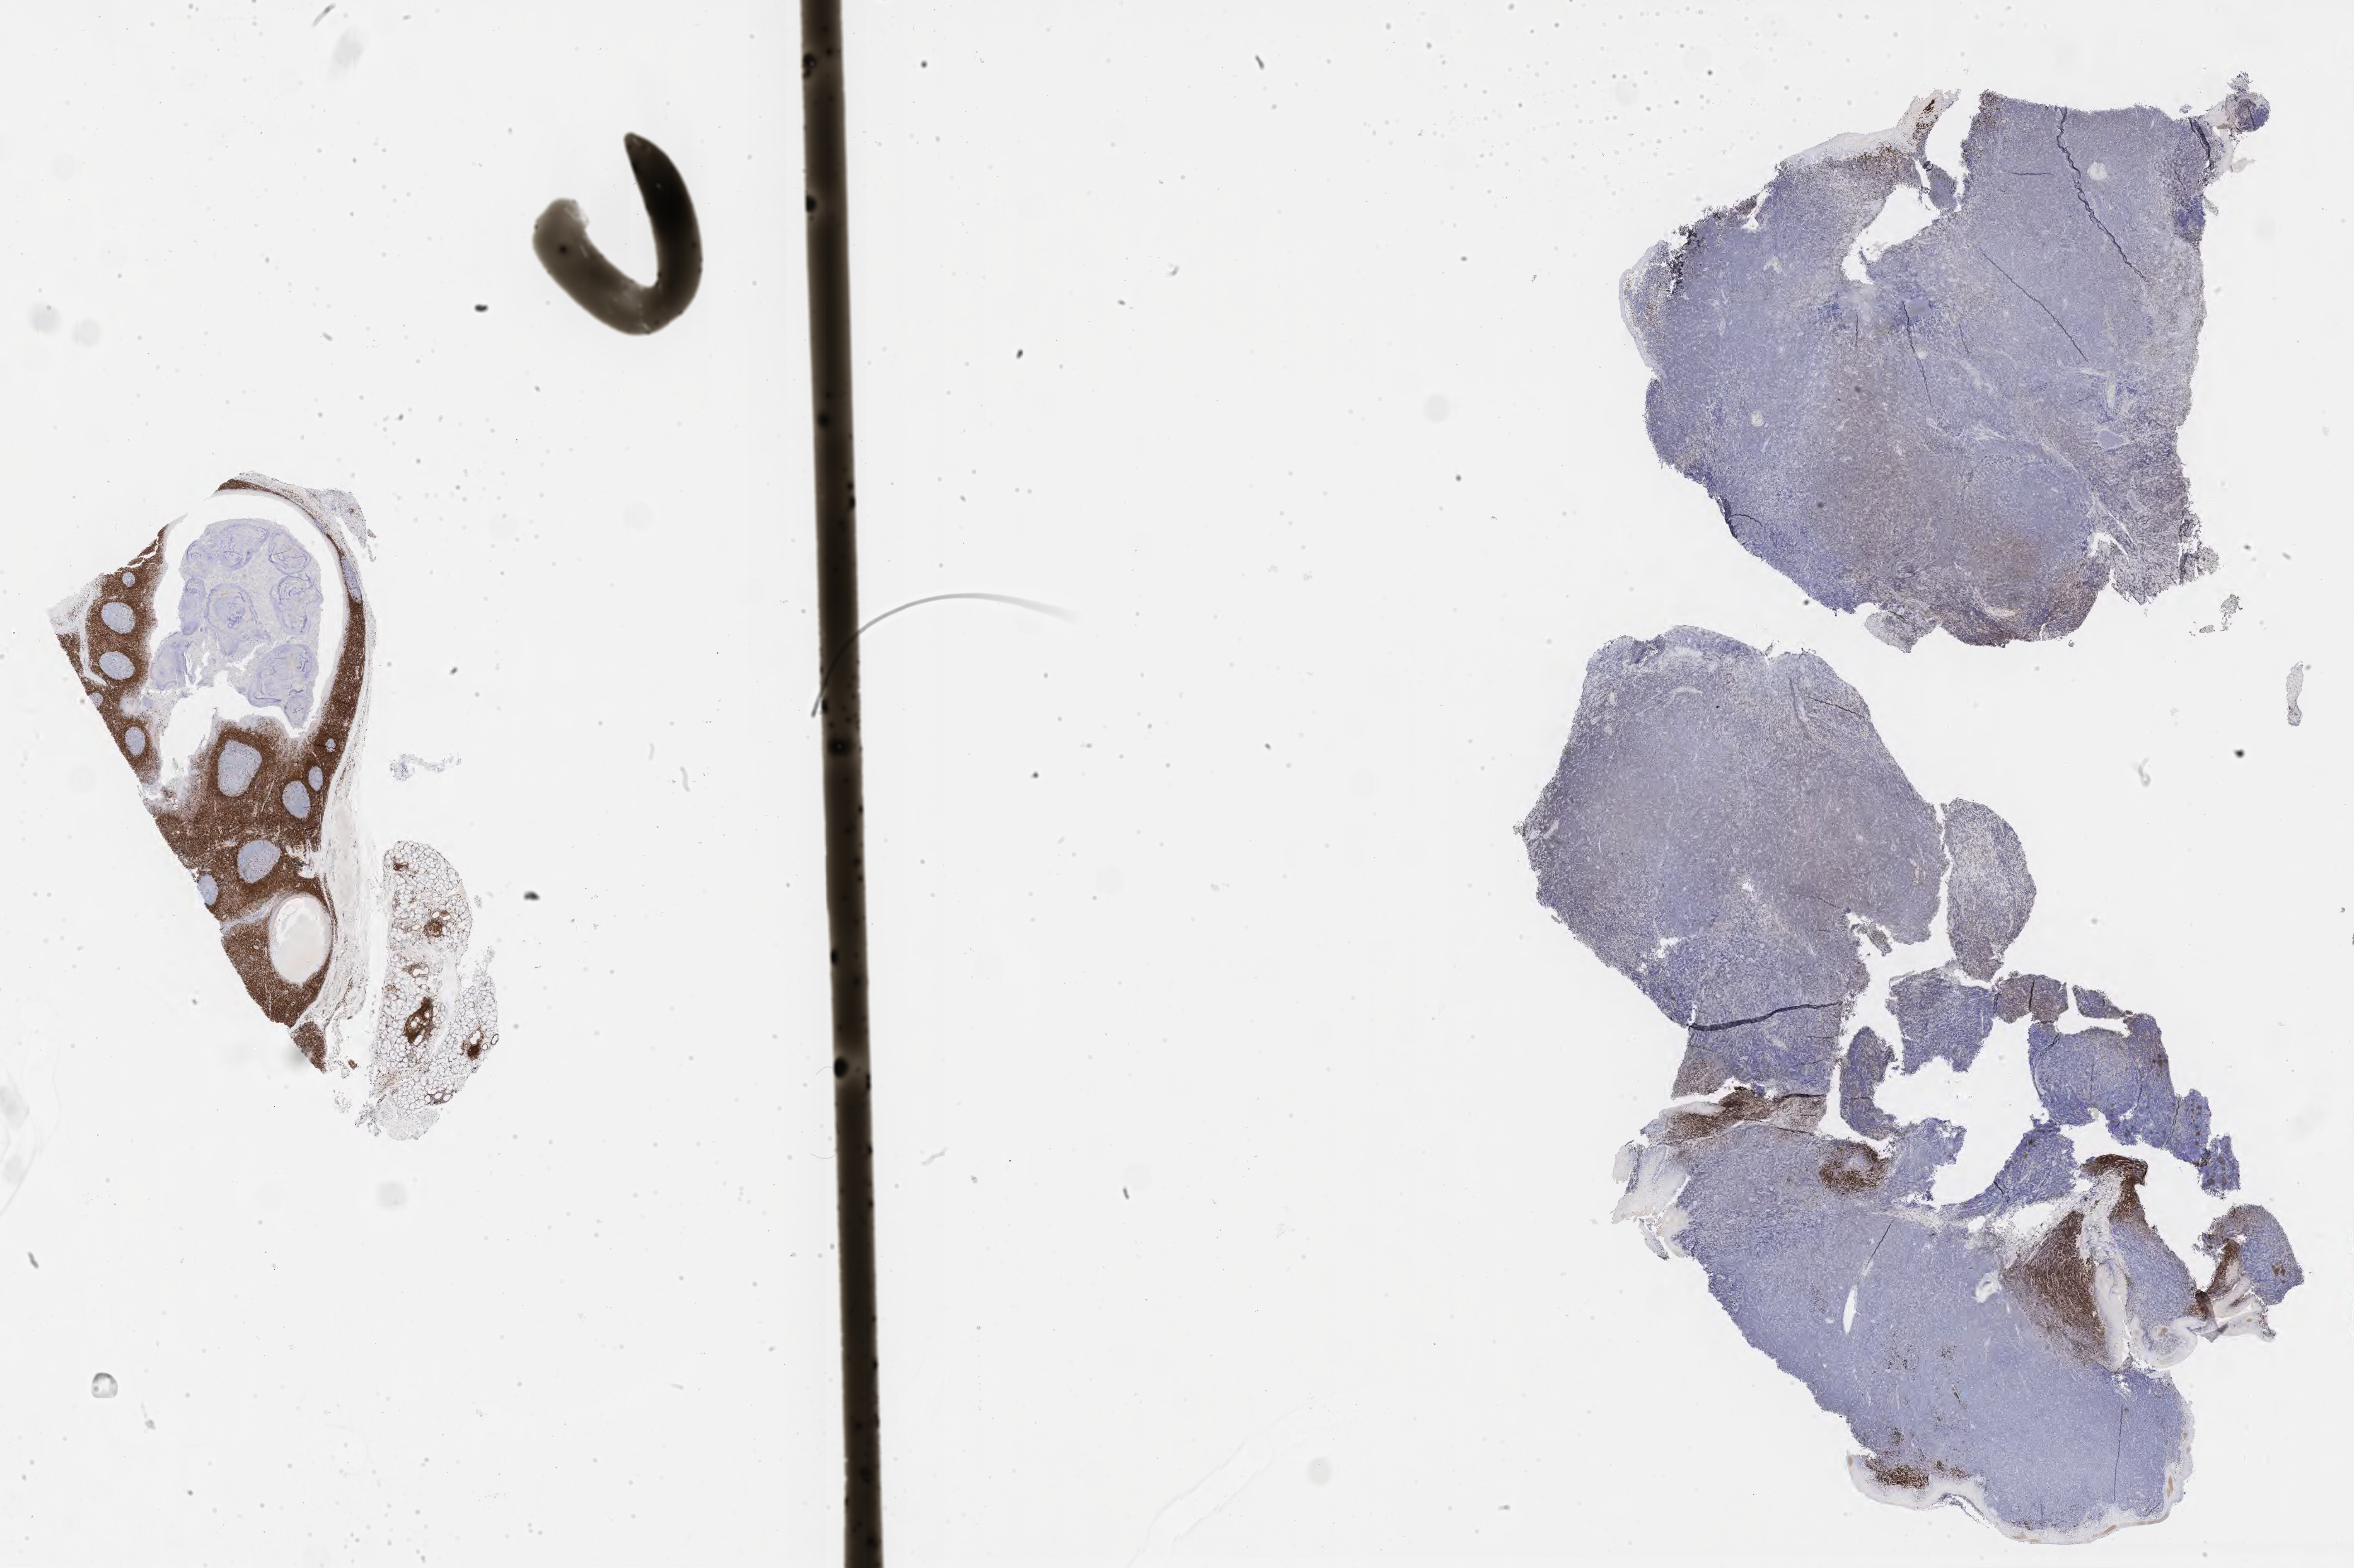
Immunohistochemistry (IHC) whole-slide image stained for BCL2, whole scanned area (about 30.2 x 20.1 mm) shown as a low-resolution overview; specimen: tumor tissue. Male patient, age 22 years.
Diagnosis: Diffuse large B-cell lymphoma, NOS.